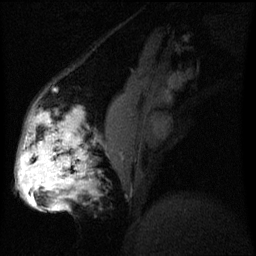
Breast MRI (dynamic contrast-enhanced), one sagittal slice. Slice 22 of 60 in the series (ordered by position). Dynamic contrast-enhanced series, image 2 of 3 at this slice position (ordered by acquisition). 1.5 T. TE 4.2 ms, TR 8 ms. 2.2 mm slice thickness. 256 × 256 image matrix, field of view 200 × 200 mm. Patient: female, 50 years.
Annotated regions visible in this slice (semi-automatic segmentation, software-assisted and operator-edited):
- analysis volume of interest (the breast-tissue region the enhancement analysis was run in; not a lesion): bounding box [x1, y1, x2, y2] px = [19, 112, 93, 211]
- tumour enhancement mask (voxels above the 70 % enhancement threshold inside the analysis volume of interest): [19, 116, 85, 211]